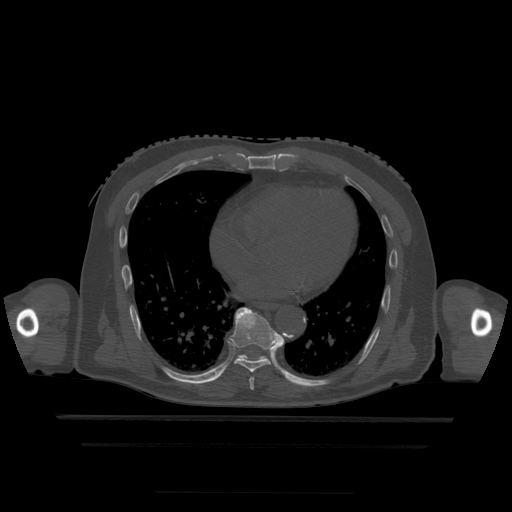
CT including the spine, one axial slice. Position 277 of 522 along the scan axis. Bone window (W 1800 / L 400 HU). 1.25 mm slice thickness. 512 × 512 image matrix. Patient age 68 years. From the clinical record (not read from this slice): primary cancer: urothelial.
Annotated regions visible in this slice (semi-automatically segmented with operator editing):
- T7 vertebra: bounding box (x1, y1, x2, y2) in pixels: (249, 378, 255, 390)
- T8 vertebra: (229, 307, 281, 373)
- T9 vertebra: (237, 355, 268, 362)